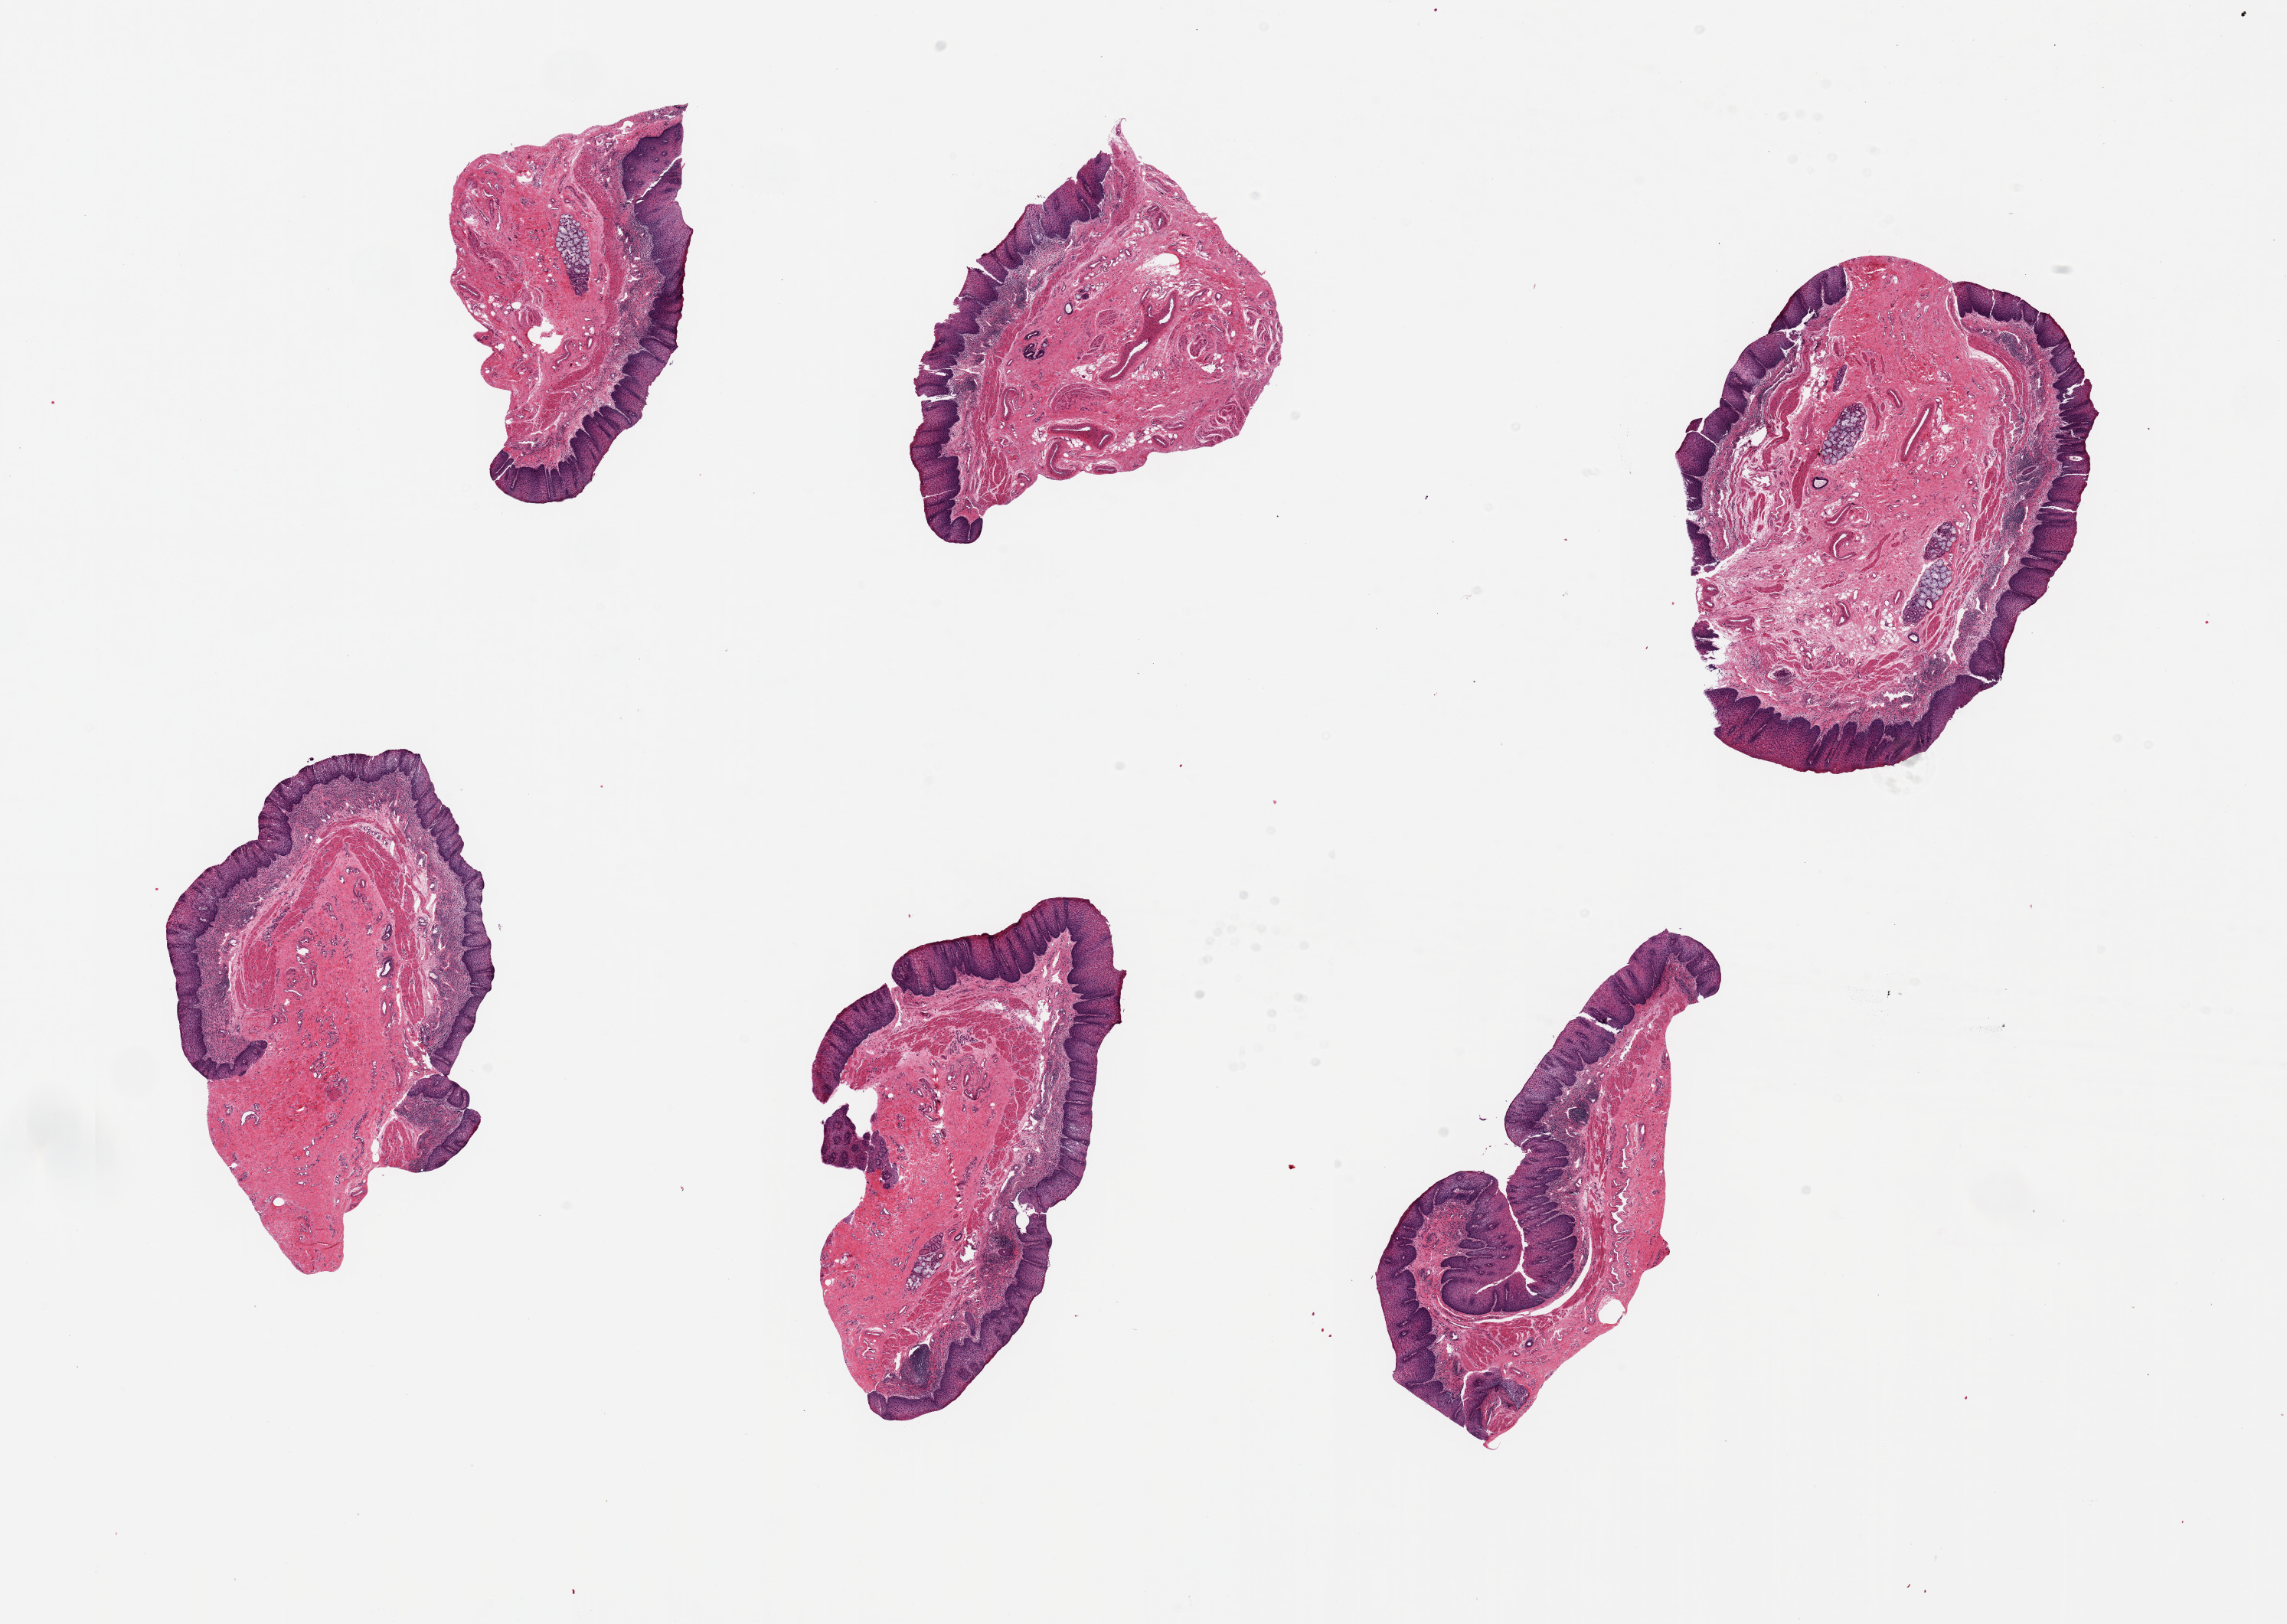
Whole-slide image, haematoxylin and eosin stain, brightfield, a low-resolution overview of the entire scanned area, about 23.6 x 16.8 mm, PAXgene-fixed, paraffin-embedded tissue, section of gastroesophageal junction (target tissue), tissue donor sample. Donor sex: male.
- reviewer comment on this tissue sample: 6 pieces ~4x3mm 10-15% squamous mucosa, numerous submucosal glands present